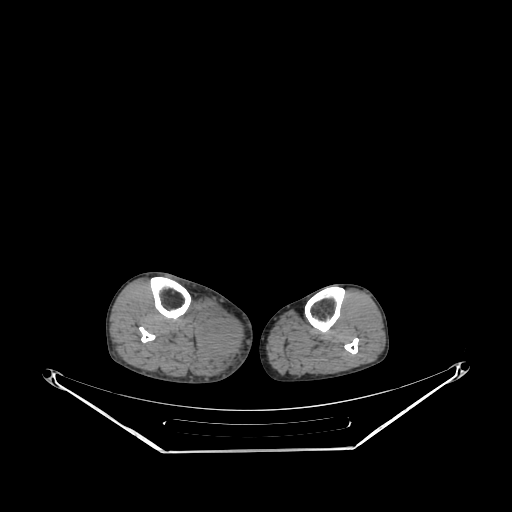
CT of an extremity soft-tissue mass (from a PET/CT study), one axial slice; slice 143 of 267 in the series (ordered by position); 140 kVp; soft-tissue window (W 400 / L 40 HU); 3.75 mm slice thickness; 512 × 512 image matrix, field of view 500 × 500 mm. Male patient. Case-level facts recorded for this patient, not image findings: histological type: pleiomorphic liposarcoma; grade: high; site of the primary tumour: right calf.
Outlined on this slice (expert contour drawn on MRI and transferred to this co-registered scan by the dataset authors):
- gross tumour volume including surrounding oedema: bounding box <199,310,243,359> (left, top, right, bottom; pixels)
- gross tumour volume (mass): <208,319,243,353>